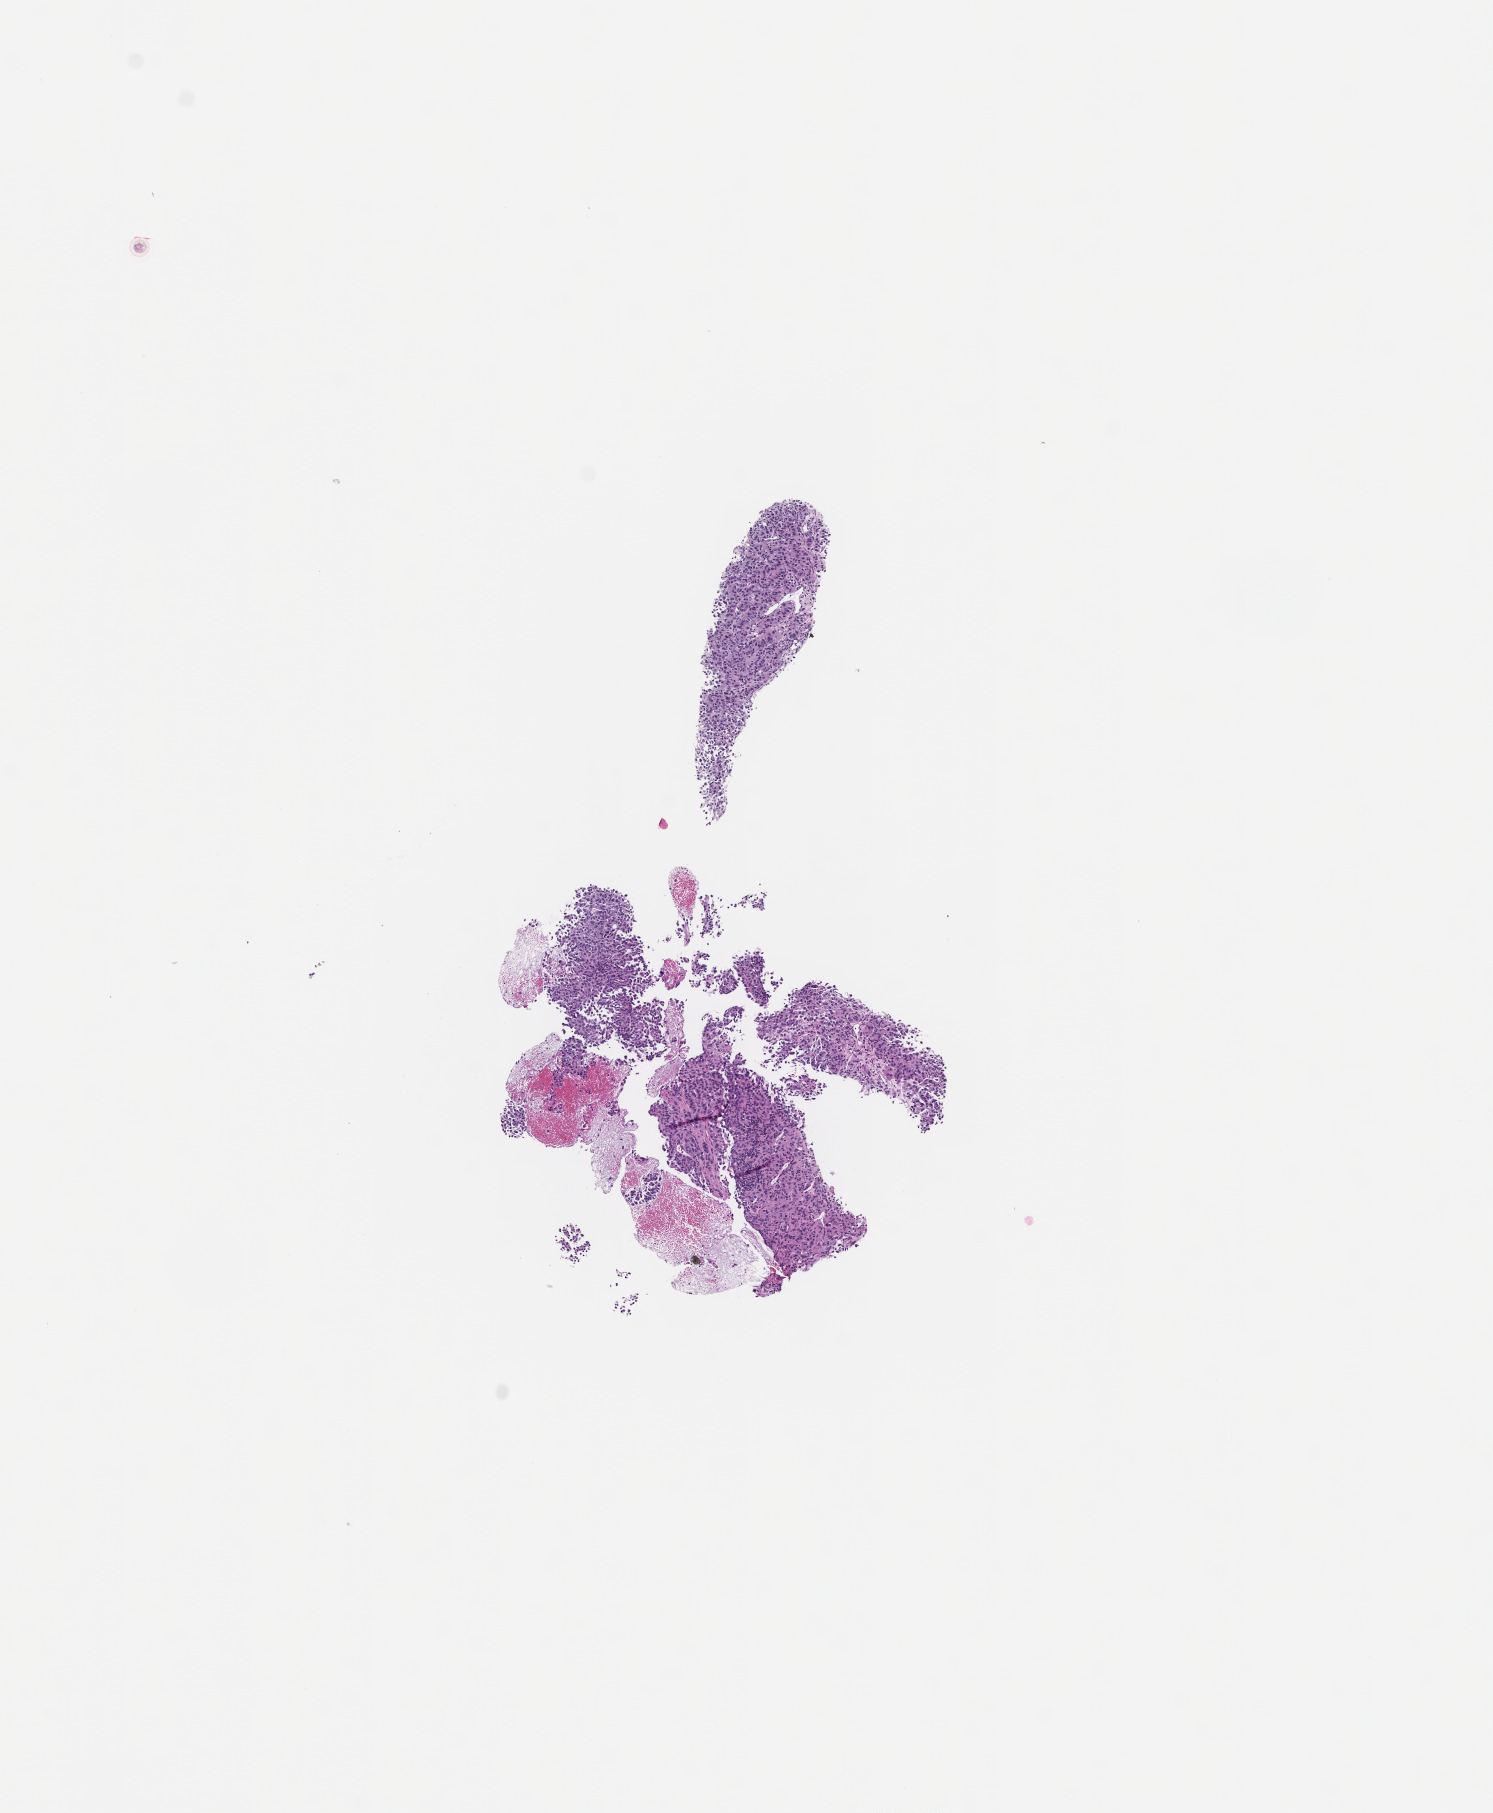
Whole-slide image, hematoxylin and eosin (H&E) stain, low-resolution overview of the scanned area, about 6.0 x 7.3 mm. Formalin-fixed, paraffin-embedded (FFPE) tissue. Specimen time point: collected at baseline (before treatment). Patient: male.
This section: metastasis (sampled organ not recorded). Primary diagnosis of the patient: Melanoma.